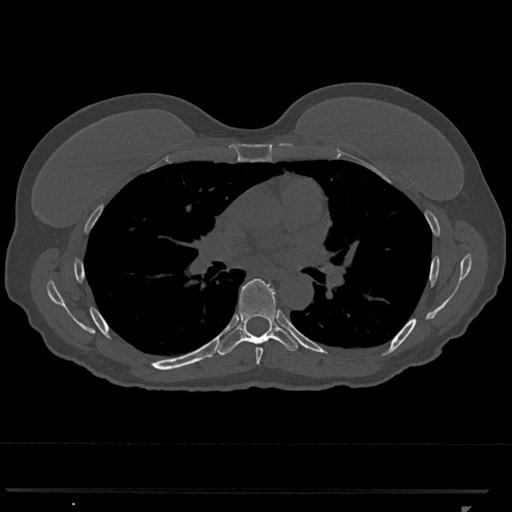
CT including the spine, one axial slice. Slice 728 of 793 in the series (ordered by position). 120 kVp. Bone window (W 1800 / L 400 HU). 0.5 mm slice thickness. 512 × 512 image matrix, field of view 380 × 380 mm. Female patient, age 62 years. From the clinical record (not read from this slice): primary cancer: renal.
Outlined on this slice (semi-automatically segmented with operator editing):
- T6 vertebra: box from (x=255, y=347) to (x=263, y=365) px
- T7 vertebra: (x=216, y=279)–(x=299, y=356)